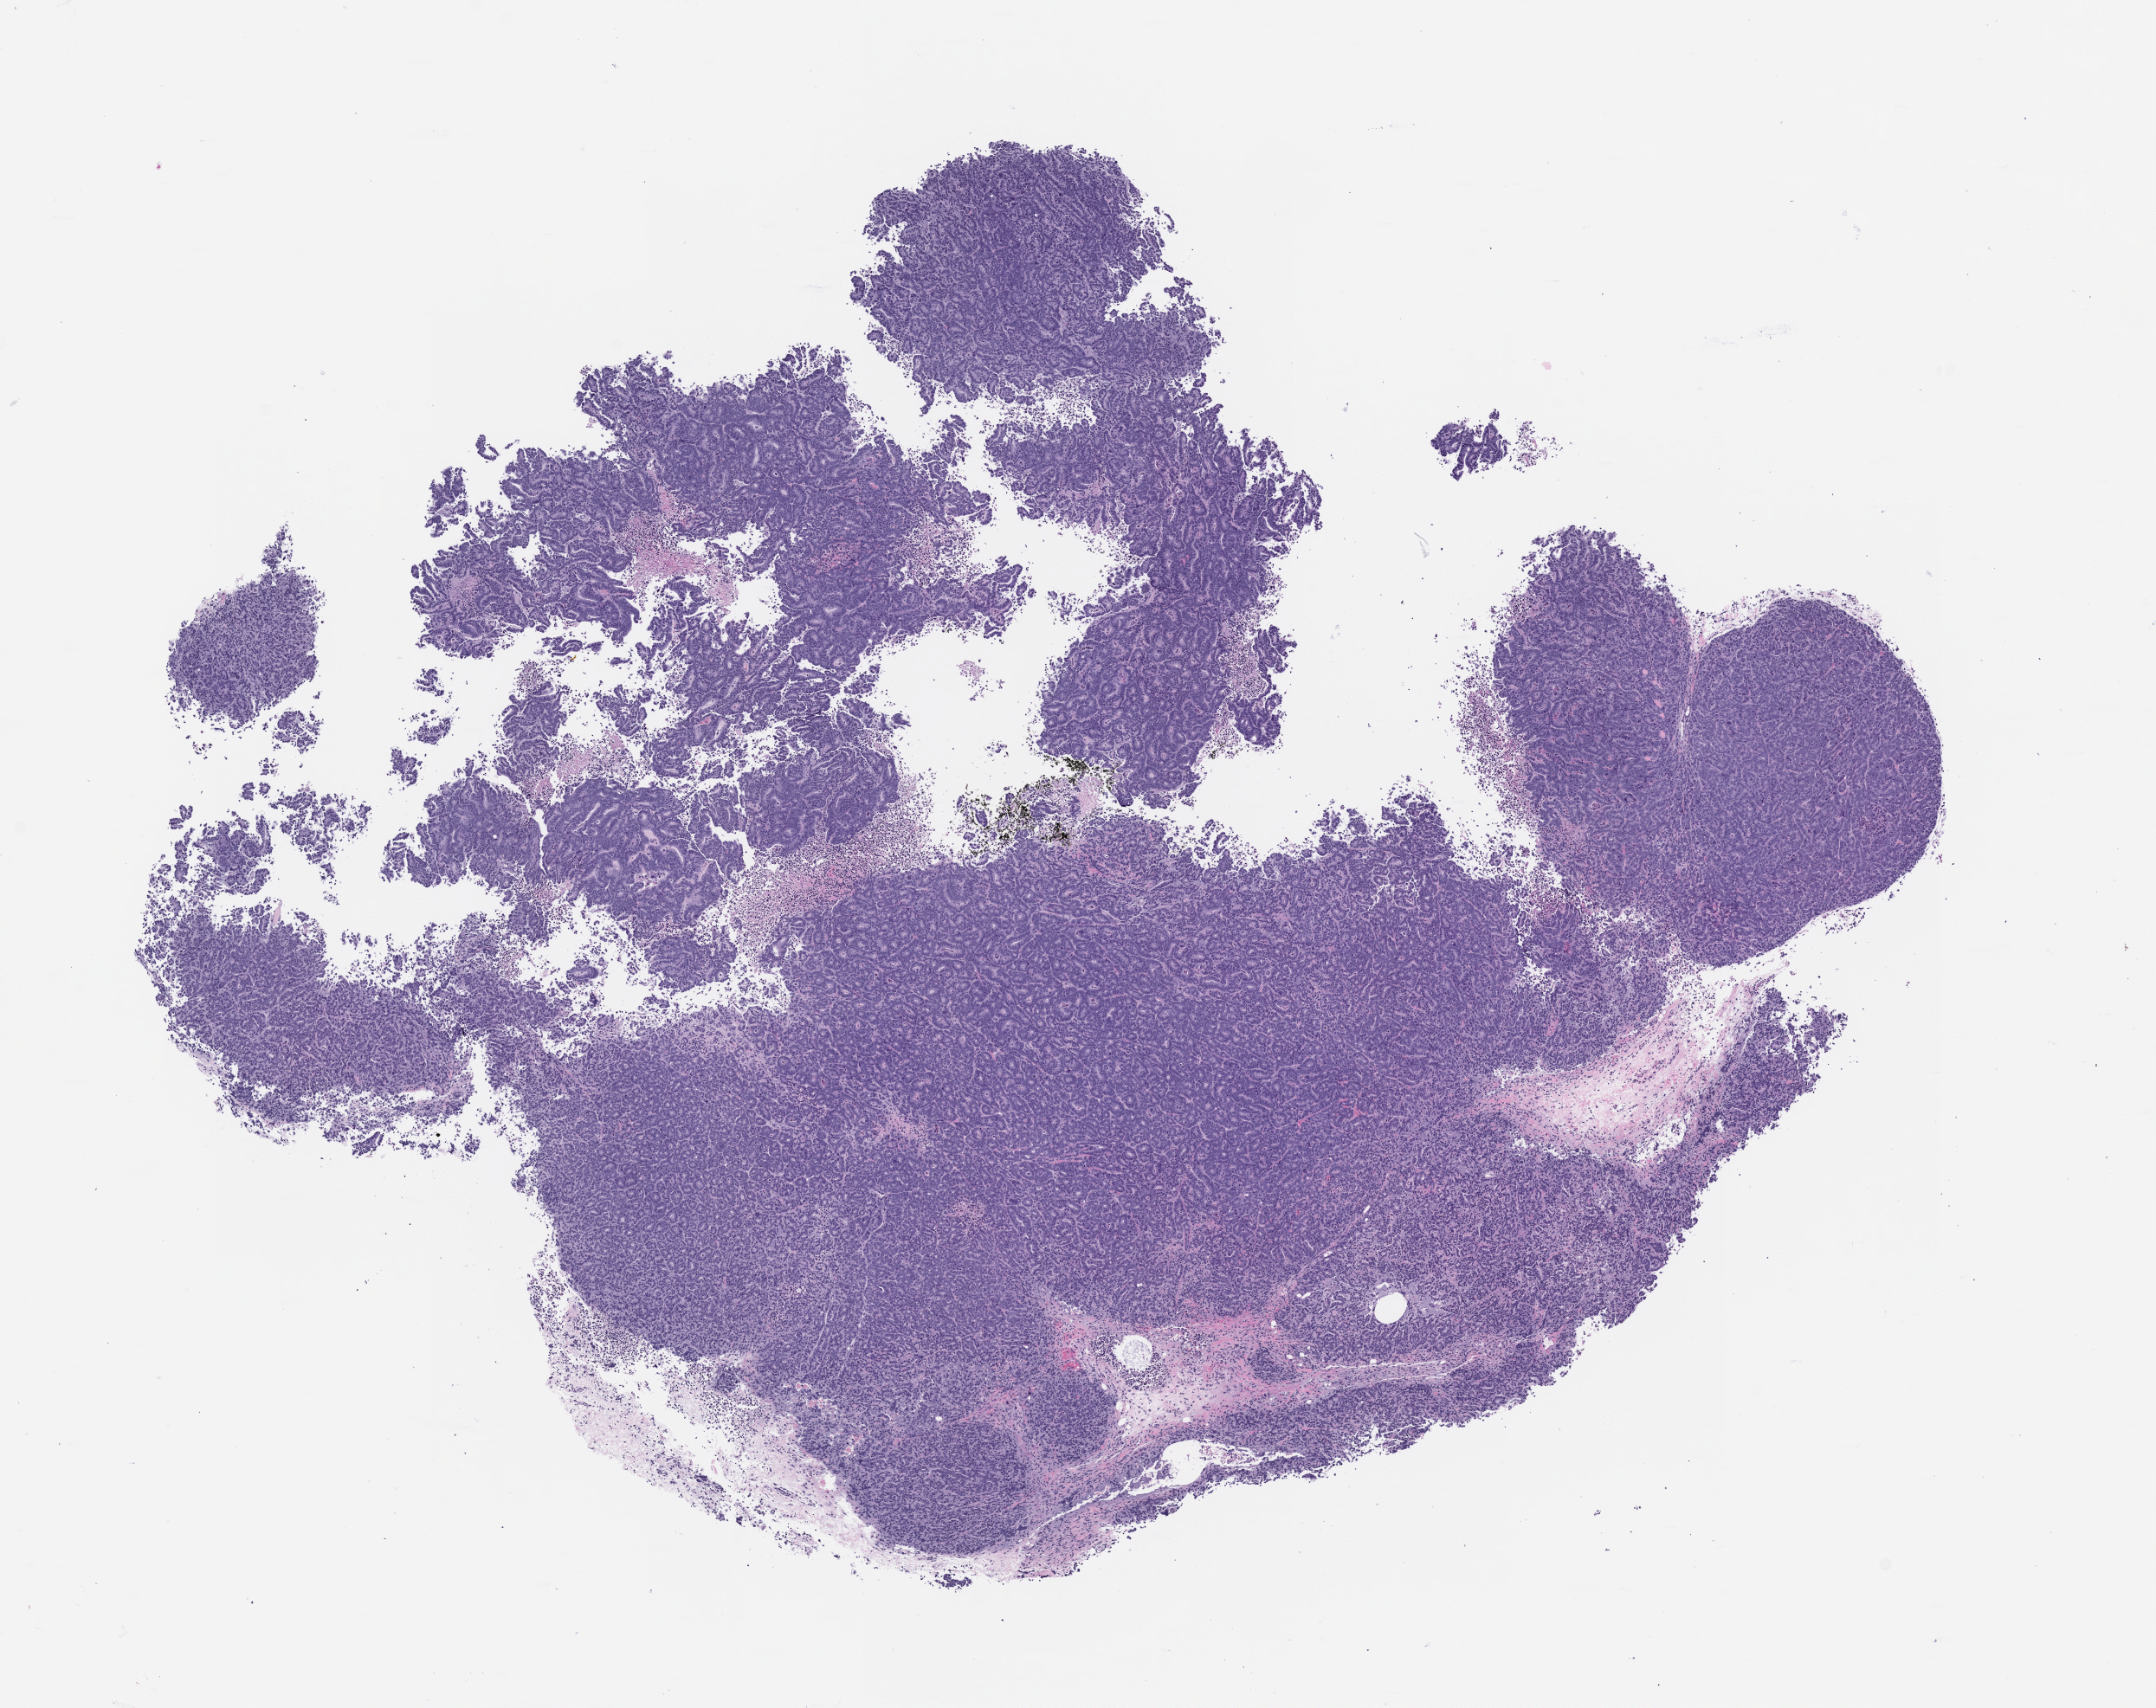
Whole-slide image, hematoxylin and eosin (H&E): patient-derived xenograft (human tumor grown in a mouse) — whole scanned area (about 10.0 x 7.9 mm) shown as a low-resolution overview, FFPE section, tumor site category: small intestine.
Originating patient diagnosis: Small Intestinal Adenocarcinoma.